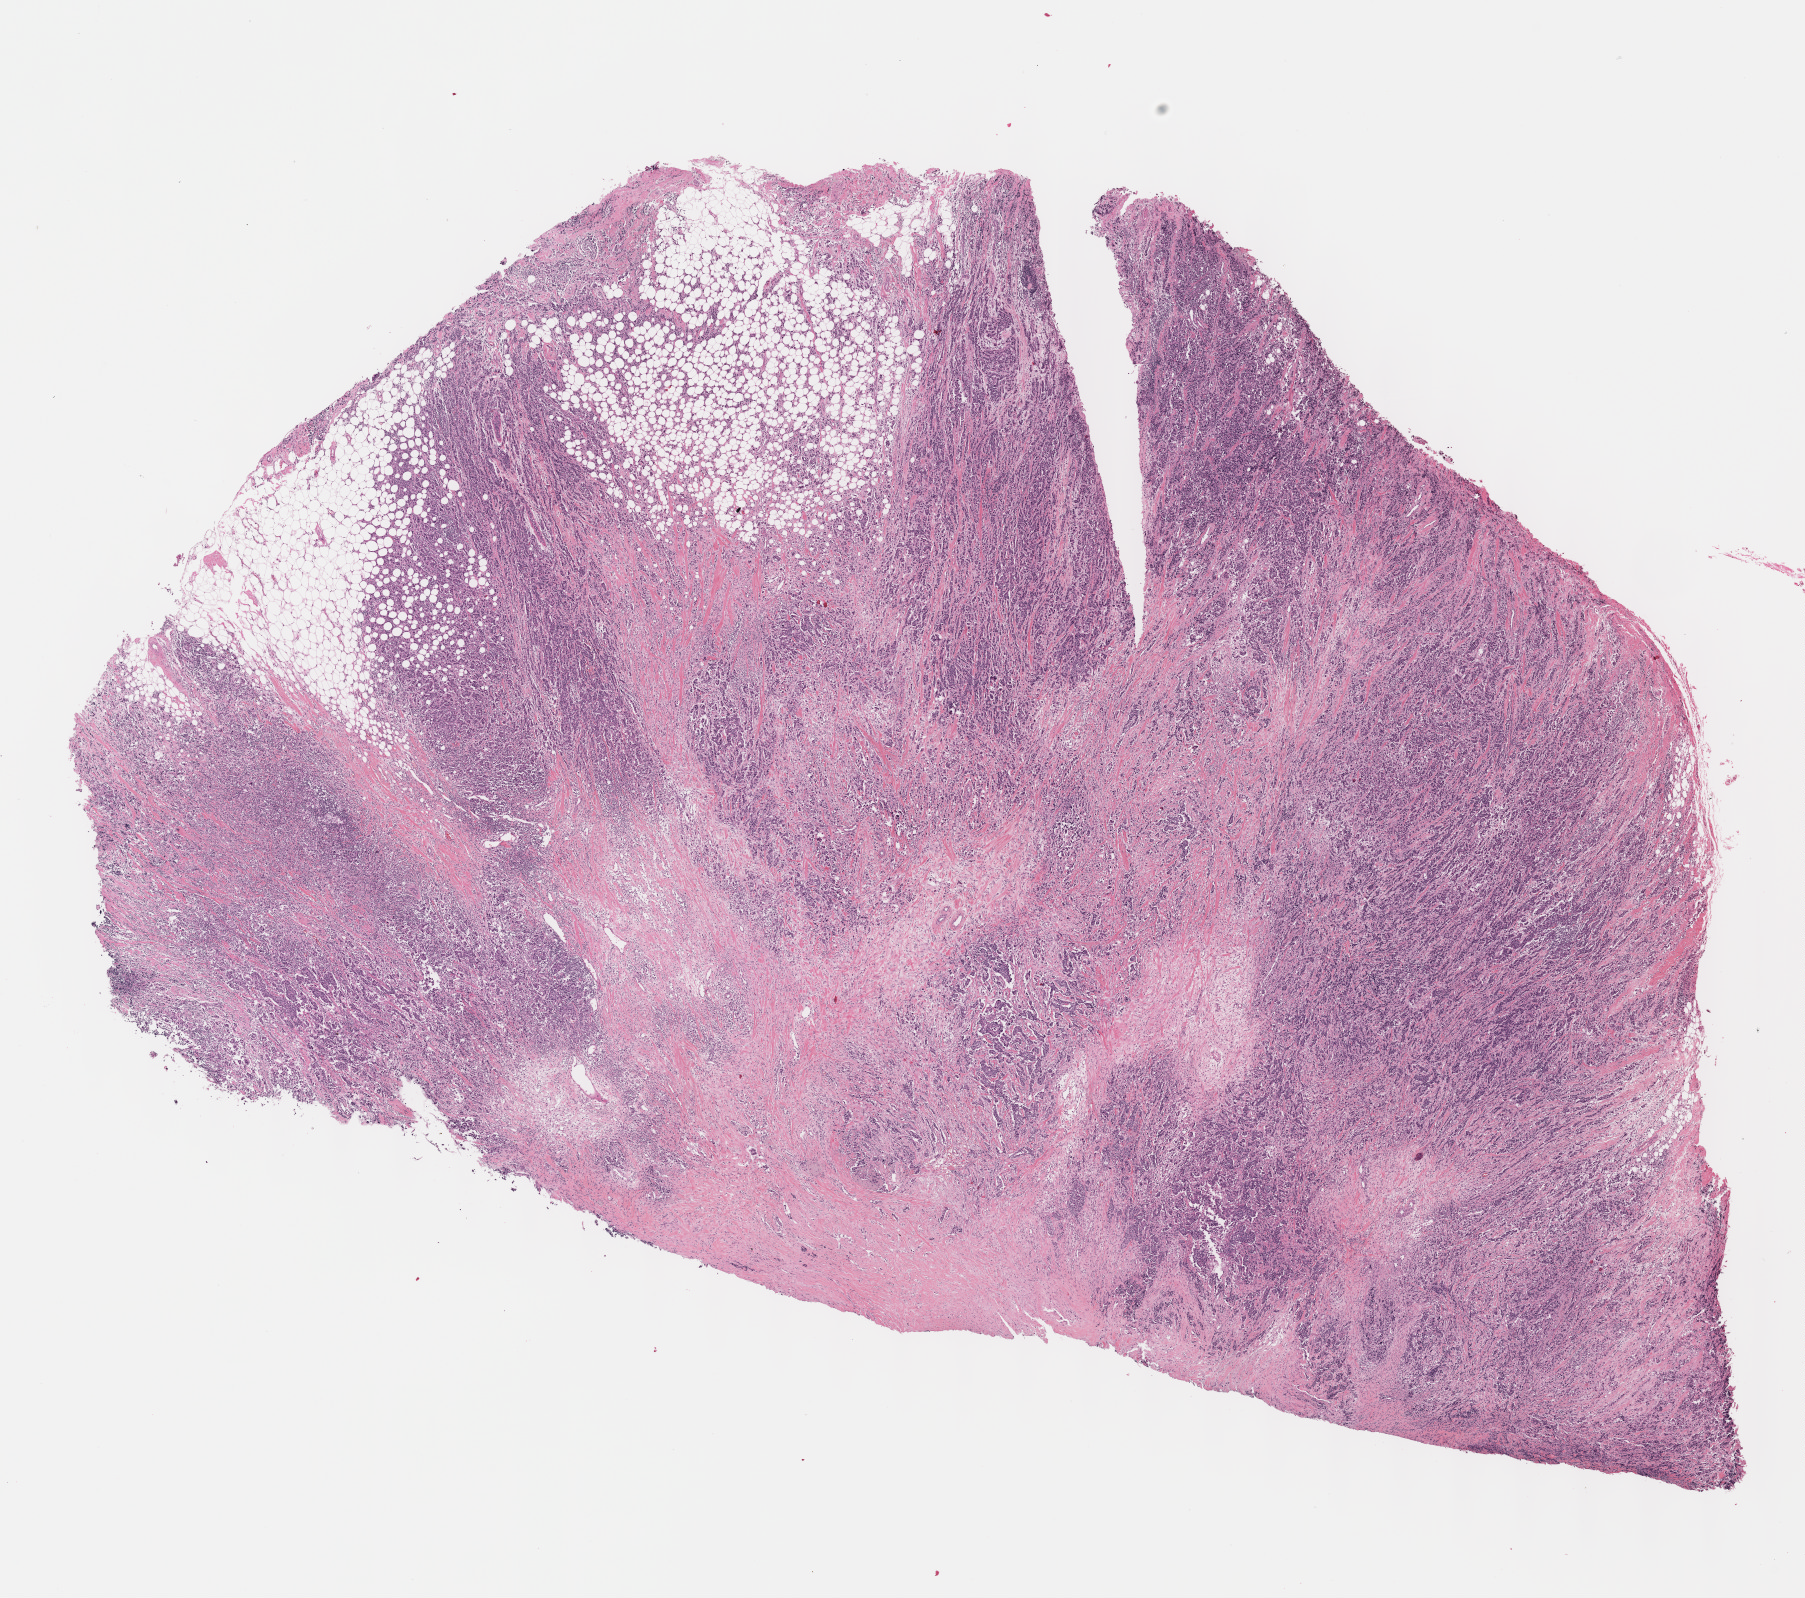
Hematoxylin and eosin (H&E) stained whole-slide image — a low-resolution overview of the entire scanned area, about 14.6 x 12.9 mm. Formalin-fixed paraffin-embedded (FFPE) diagnostic section. Primary tumour sample from the breast. Female, age 68 years at initial diagnosis.
Diagnosis: Infiltrating duct carcinoma, NOS. Laterality: right. Lymph nodes positive (case pathology): 1 of 15 examined. AJCC pathologic stage: IIIA (7th edition). TNM: T2 N2 M0.